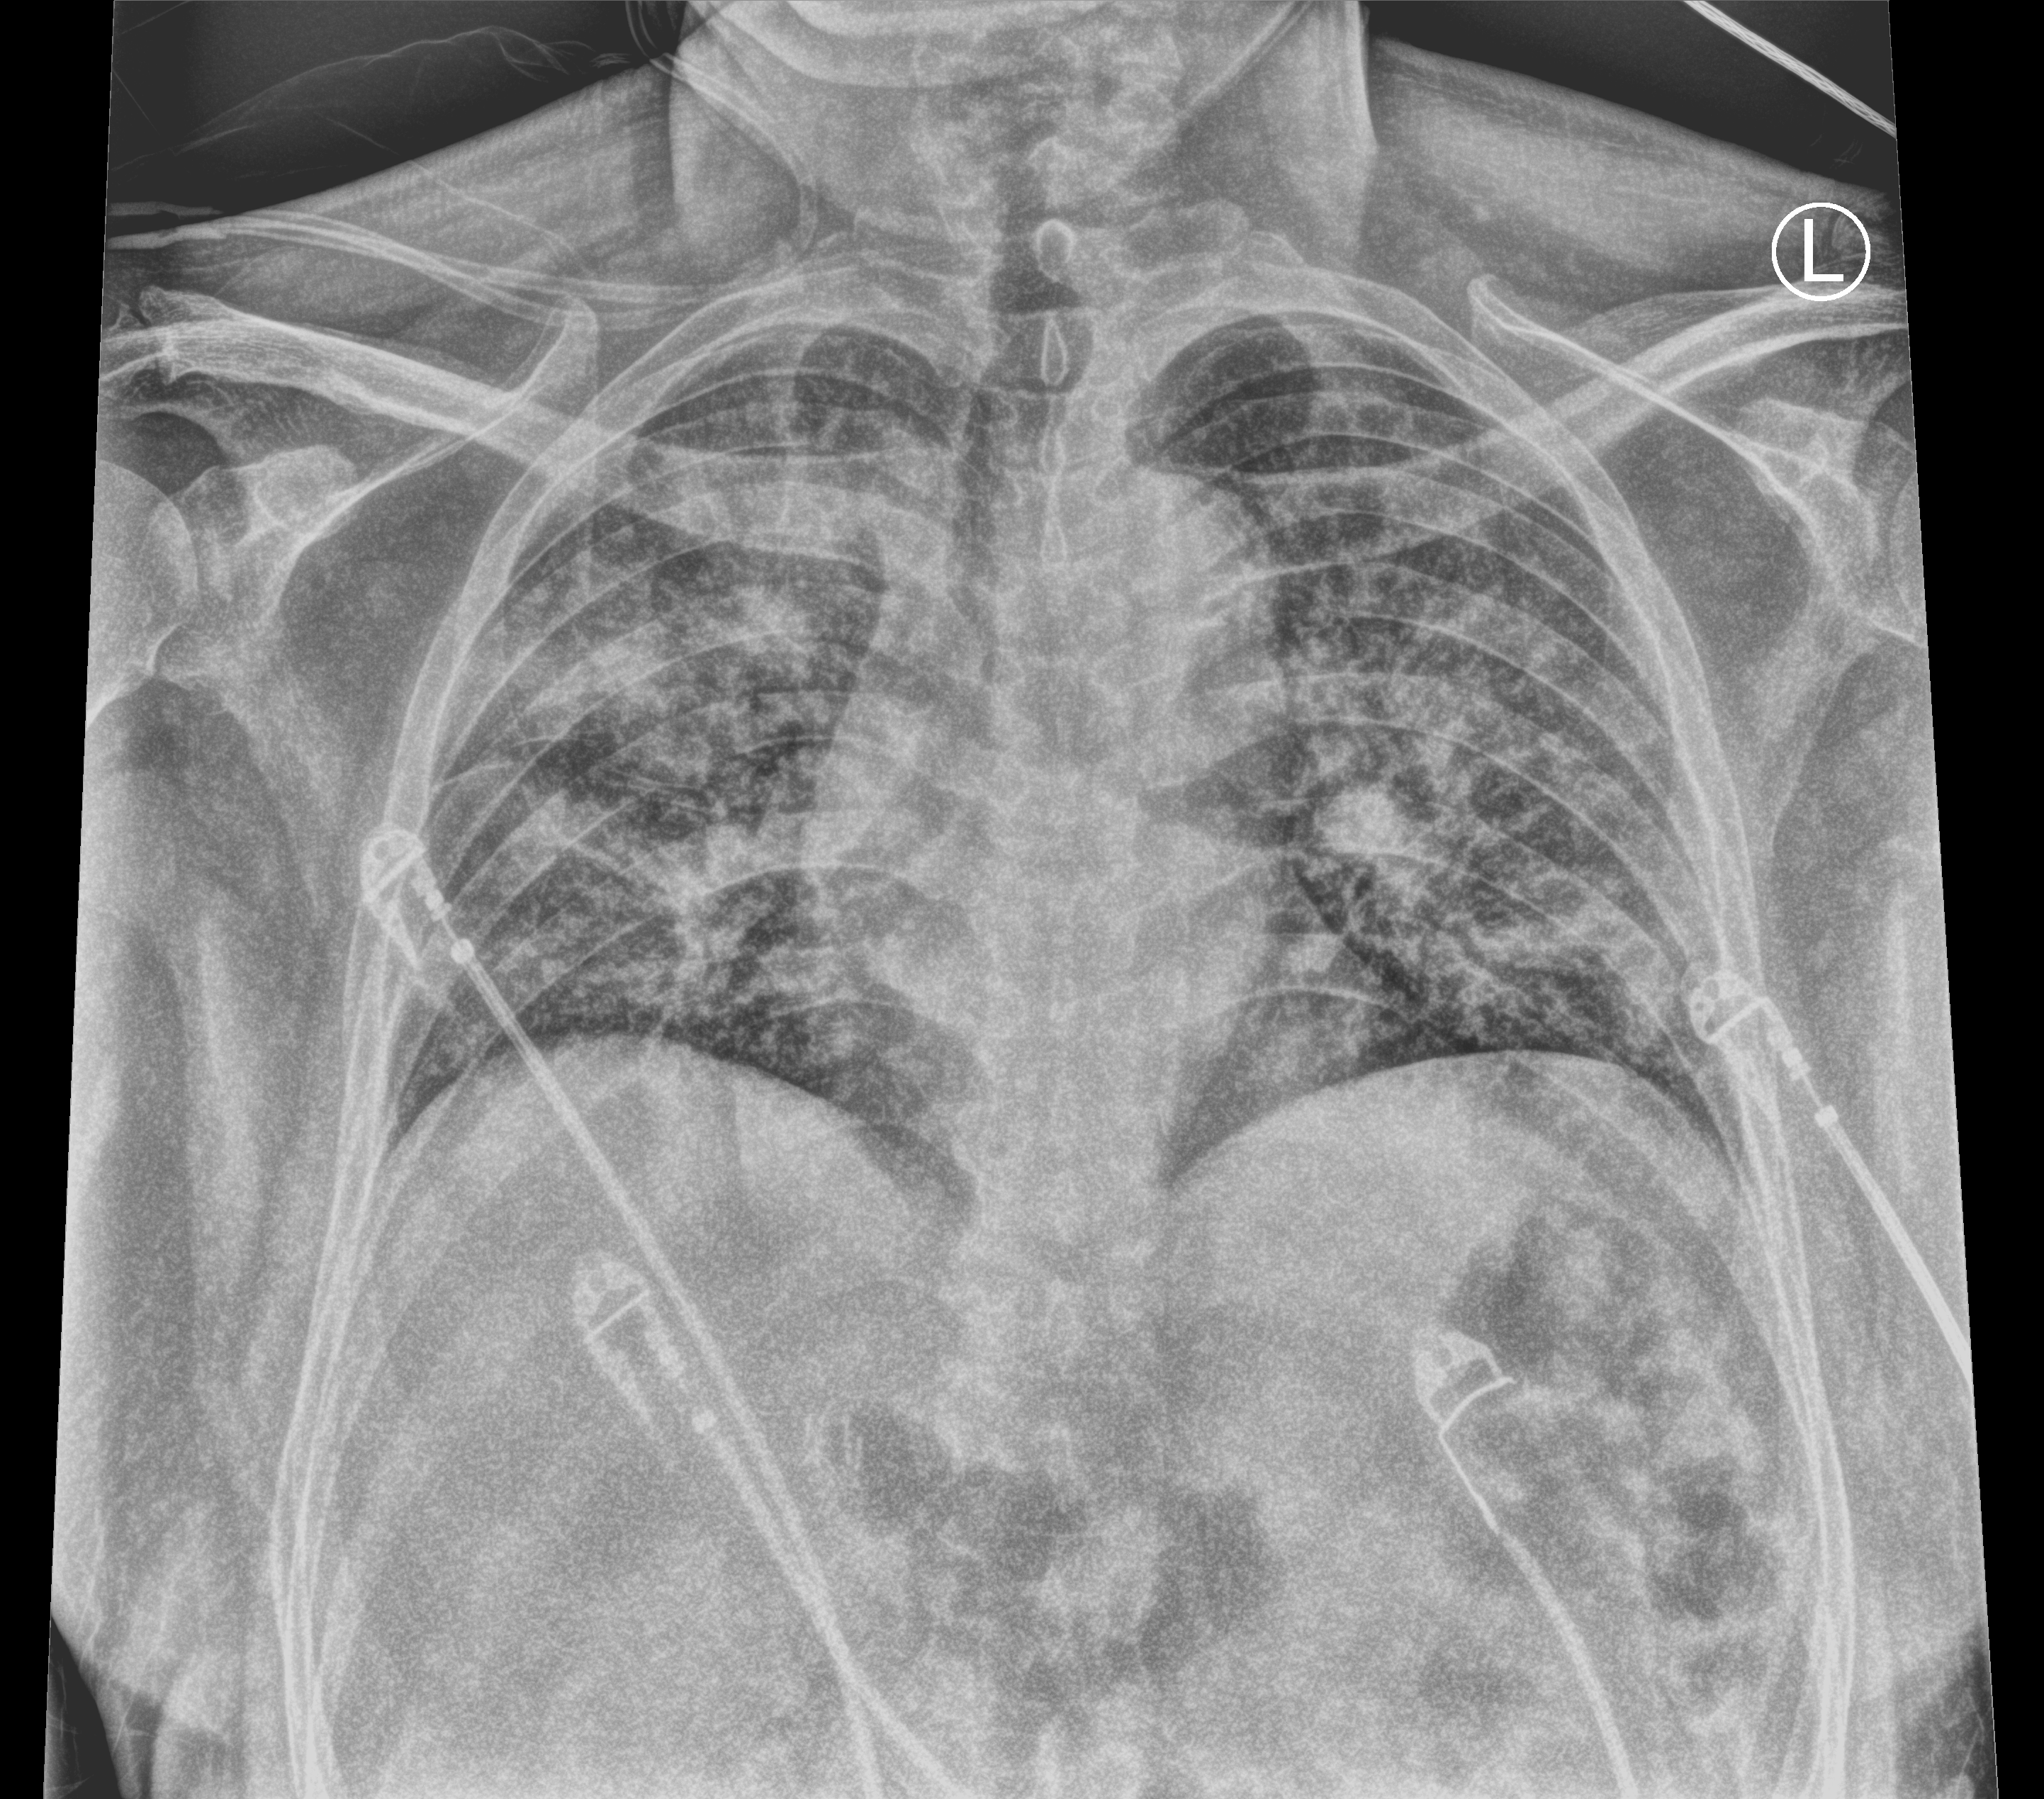
Bedside chest radiograph (computed radiography). Male patient hospitalised with COVID-19, age 60–74 years.
From the hospital-stay record, not from the radiograph (when in the stay this image was taken is not recorded):
- other chronic lung disease (admission record): no